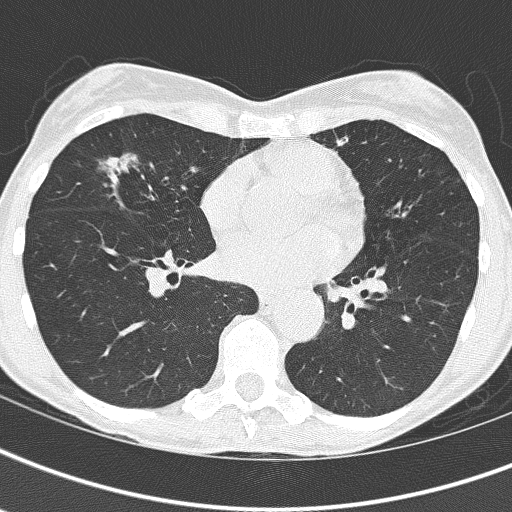
Low-dose screening chest CT, axial slice. Baseline screening round. Lung window (W 1500 / L -600 HU). 2 mm slice thickness. 120 kVp. Slice 93 of 161 in the series. 512 × 512 image matrix. Female, age 67 years at enrolment.
- Lesion marked by an expert reader, bounding box <89,134,177,214> (left, top, right, bottom; pixels).
- No non-calcified nodule or mass ≥4 mm was recorded by the screening reader at this exam.
- Lung cancer was diagnosed 832 days after this screen (after the third annual screen): bronchiolo-alveolar adenocarcinoma, NOS, right middle lobe, well differentiated (G1), stage IA (AJCC 6th edition), 25 mm at pathology.